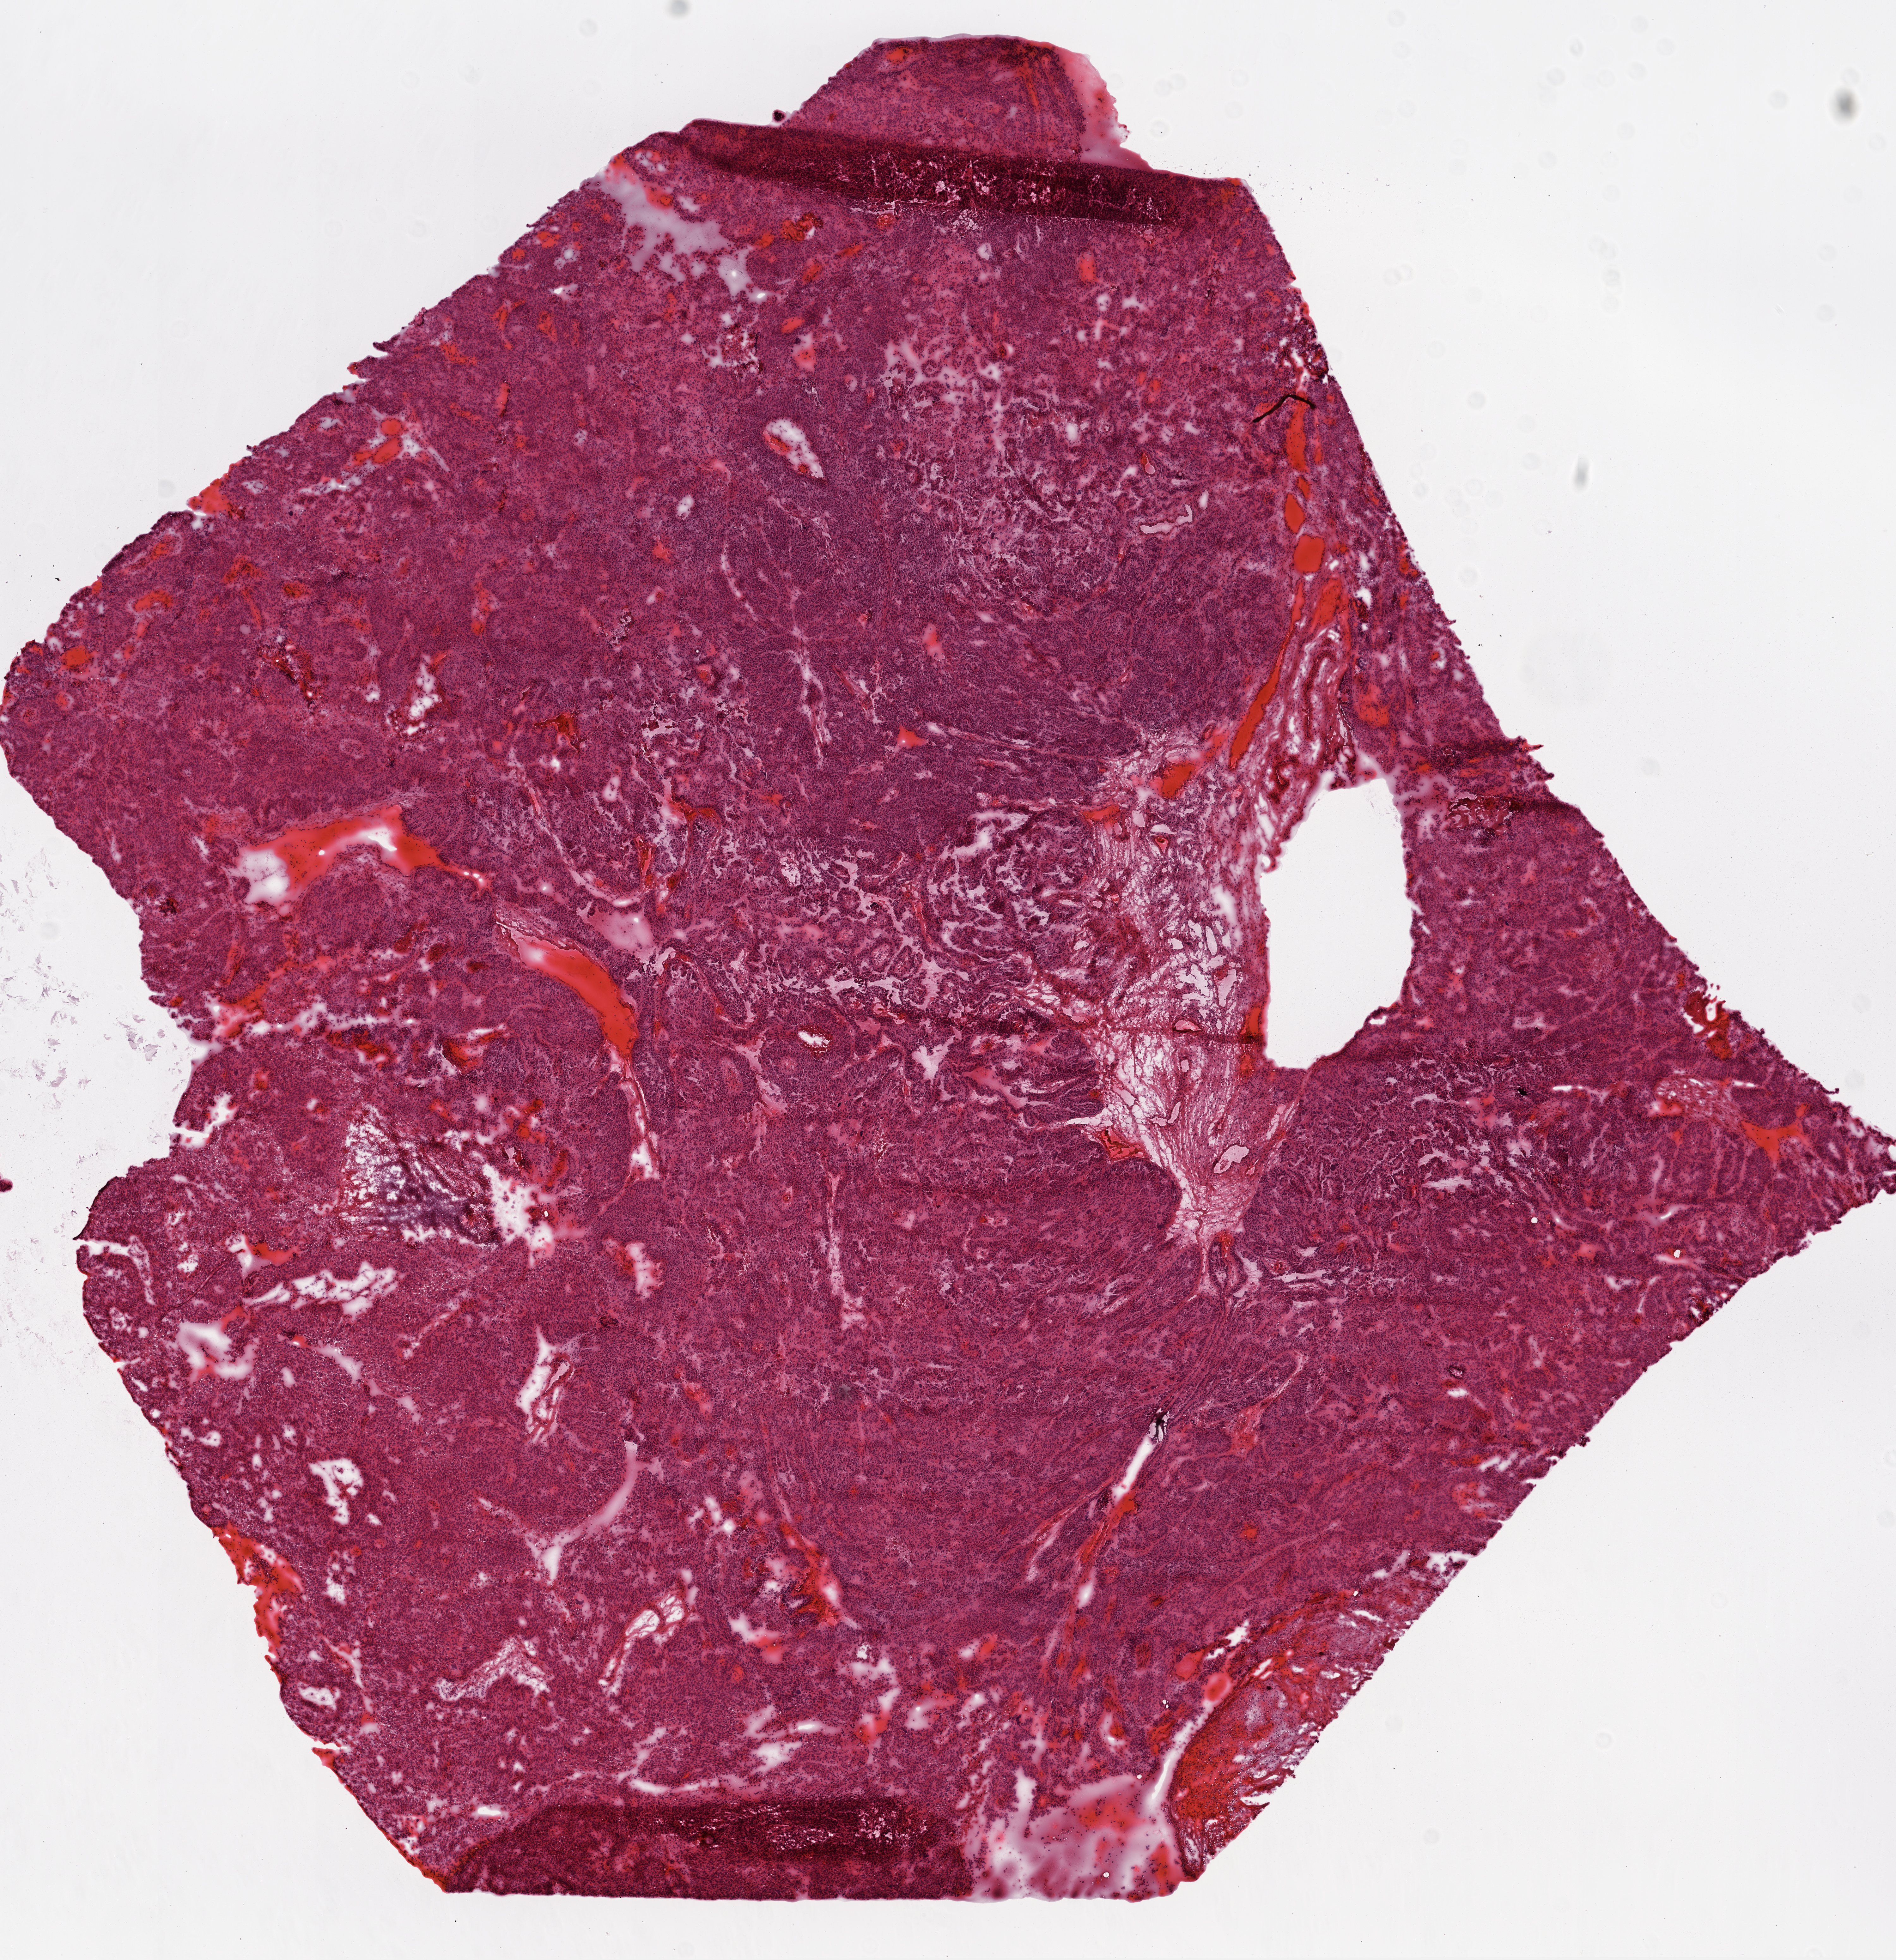
Digitized H&E tissue section (whole slide) — a low-resolution overview of the entire scanned area, about 12.0 x 12.4 mm (acquisition: 20x scan), frozen section from the top of the tissue portion, ovary, primary tumour sample. Patient: female, age at initial diagnosis 53 years. Histologic grade: G3 (poorly differentiated). Composition of this section per pathologist review: tumour cells 87%, tumour nuclei 95%, normal cells 8%, stromal cells 0%, necrosis 5%.
Diagnosis: Serous cystadenocarcinoma, NOS. FIGO stage: IIIB.